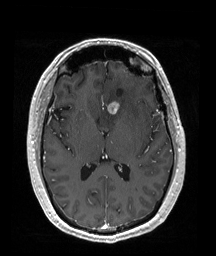
Brain MRI from a brain-tumour surgery series, one axial slice. Slice 93 of 192 in the series (ordered by position). T1-weighted post-contrast. 216 × 256 image matrix, field of view 211 × 250 mm. Case-level facts recorded for this patient, not image findings: histopathology: Oligodendroglioma; WHO grade: 2; IDH mutation: yes; tumour location: Left Frontal (septal).
Structures marked on this image (expert manual segmentation):
- tumour: box from (x=107, y=100) to (x=132, y=114) px